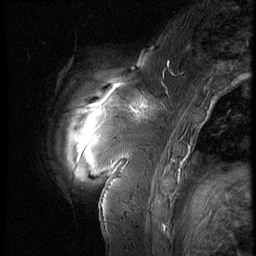
Breast MRI (dynamic contrast-enhanced), one sagittal slice. Position 13 of 60 along the scan axis. 3 images stored at this slice position (order not interpretable as contrast timing). 1.5 T. TE 4.2 ms, TR 9 ms. 2.5 mm slice thickness. 256 × 256 image matrix, field of view 180 × 180 mm. Patient: female, 57 years. Case-level facts recorded for this patient, not image findings: setting: breast cancer imaged before/during neoadjuvant chemotherapy; receptor status: triple-negative.
Structures marked on this image (semi-automatically segmented with operator editing):
- analysis volume of interest (the breast-tissue region the enhancement analysis was run in; not a lesion): bounding box [x1, y1, x2, y2] px = [114, 83, 170, 131]
- tumour enhancement mask (voxels above the 140 % enhancement threshold inside the analysis volume of interest): [115, 85, 147, 114]